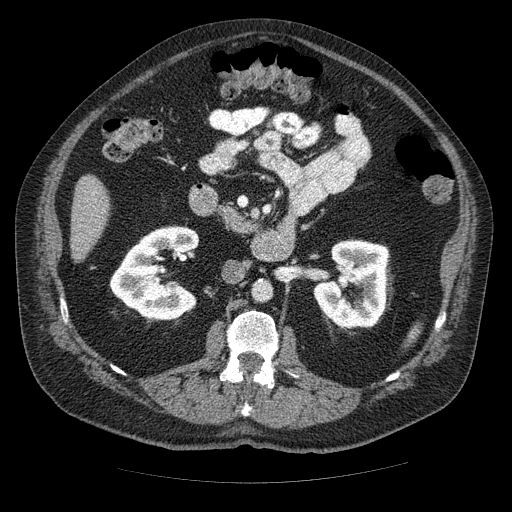
Contrast-enhanced abdominal CT (liver protocol), one axial slice; slice 10 of 85 in the series (ordered by position); reconstruction kernel STANDARD; 120 kVp; soft-tissue window (W 400 / L 40 HU); 512 × 512 image matrix, field of view 420 × 420 mm. Case-level facts recorded for this patient, not image findings: diagnosis: hepatocellular carcinoma (patient treated with transarterial chemoembolisation; whether this scan precedes or follows treatment is not stated here); TNM stage (as recorded): Stage-IIIA; Child-Pugh class: A; tumour nodularity: multinodular.
Structures marked on this image (semi-automatically segmented with operator editing):
- liver parenchyma outside the tumour (the mass and vessels are separate outlines, so this box may not span the whole liver): bounding box <70,175,110,260> (left, top, right, bottom; pixels)